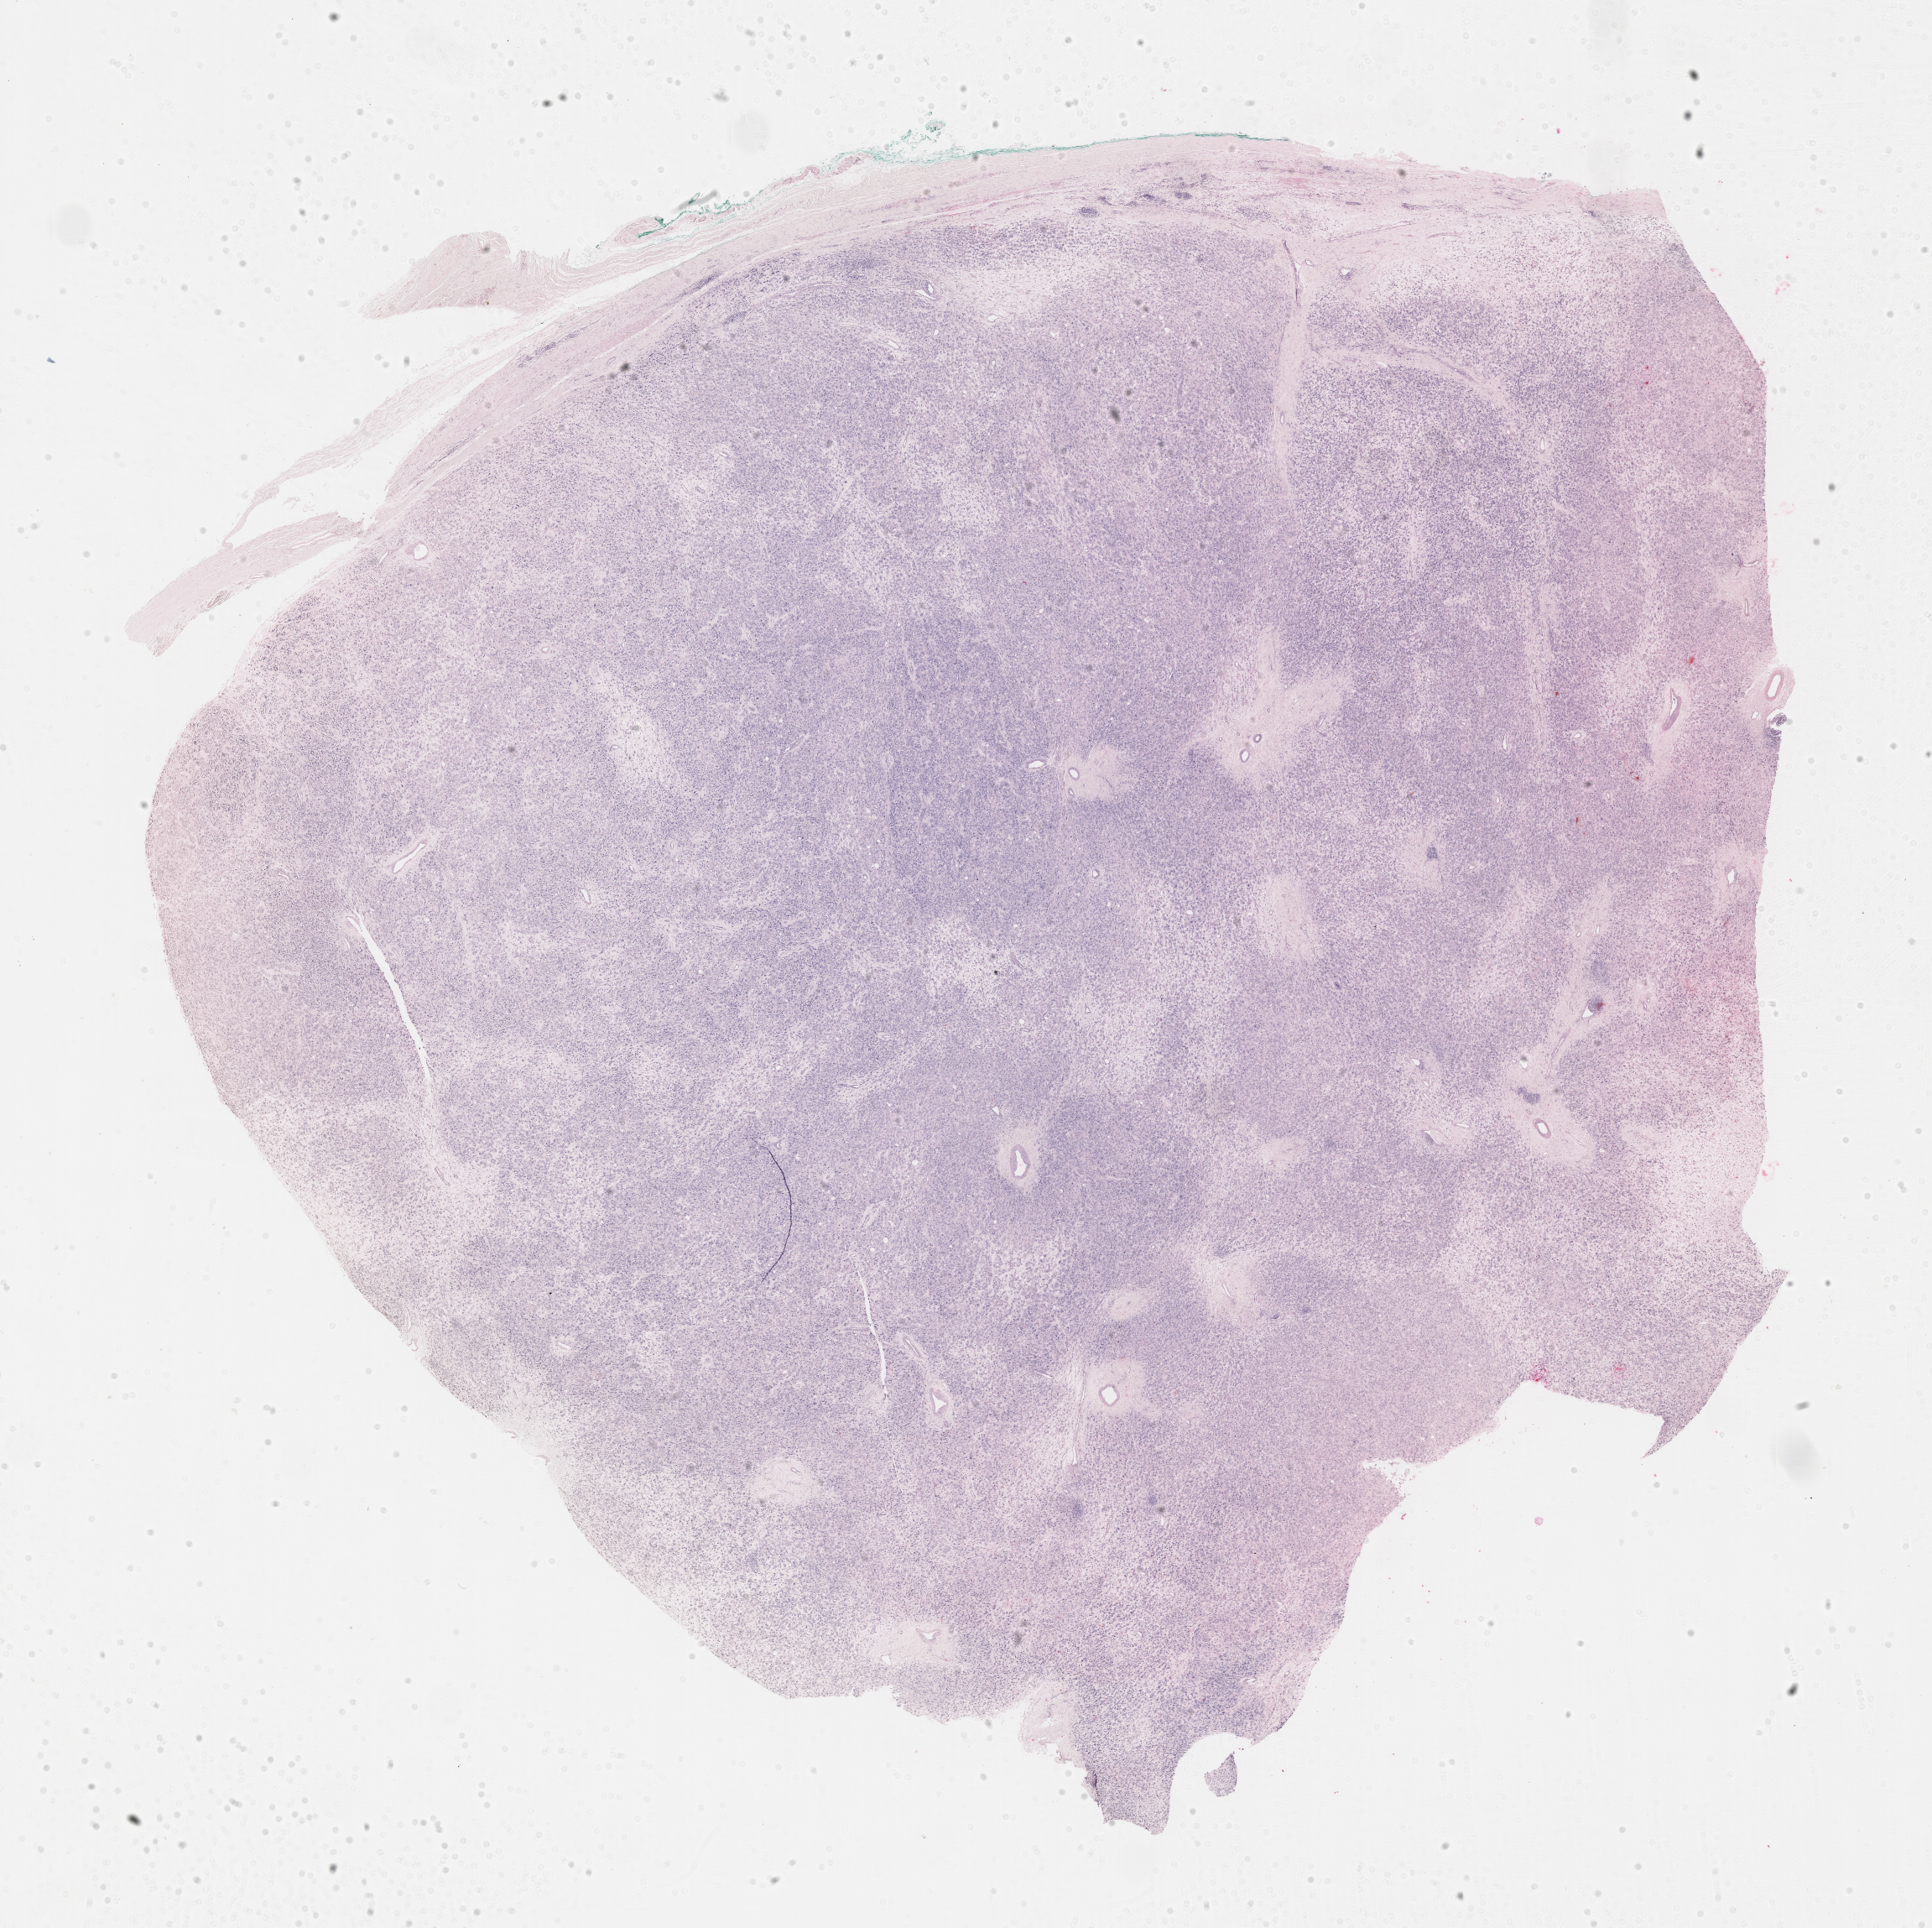
Digitized haematoxylin and eosin-stained section of tumor tissue — a low-resolution overview of the entire scanned area, about 18.6 x 18.6 mm, formalin-fixed paraffin-embedded section, sample anatomic site: testicle, left. Patient: male, age 8.1 years at diagnosis.
Stage (as recorded): 1. Diagnosis: rhabdomyosarcoma; histological classification: embryonal rhabdomyosarcoma. Metastatic status at presentation (as recorded): non-metastatic.